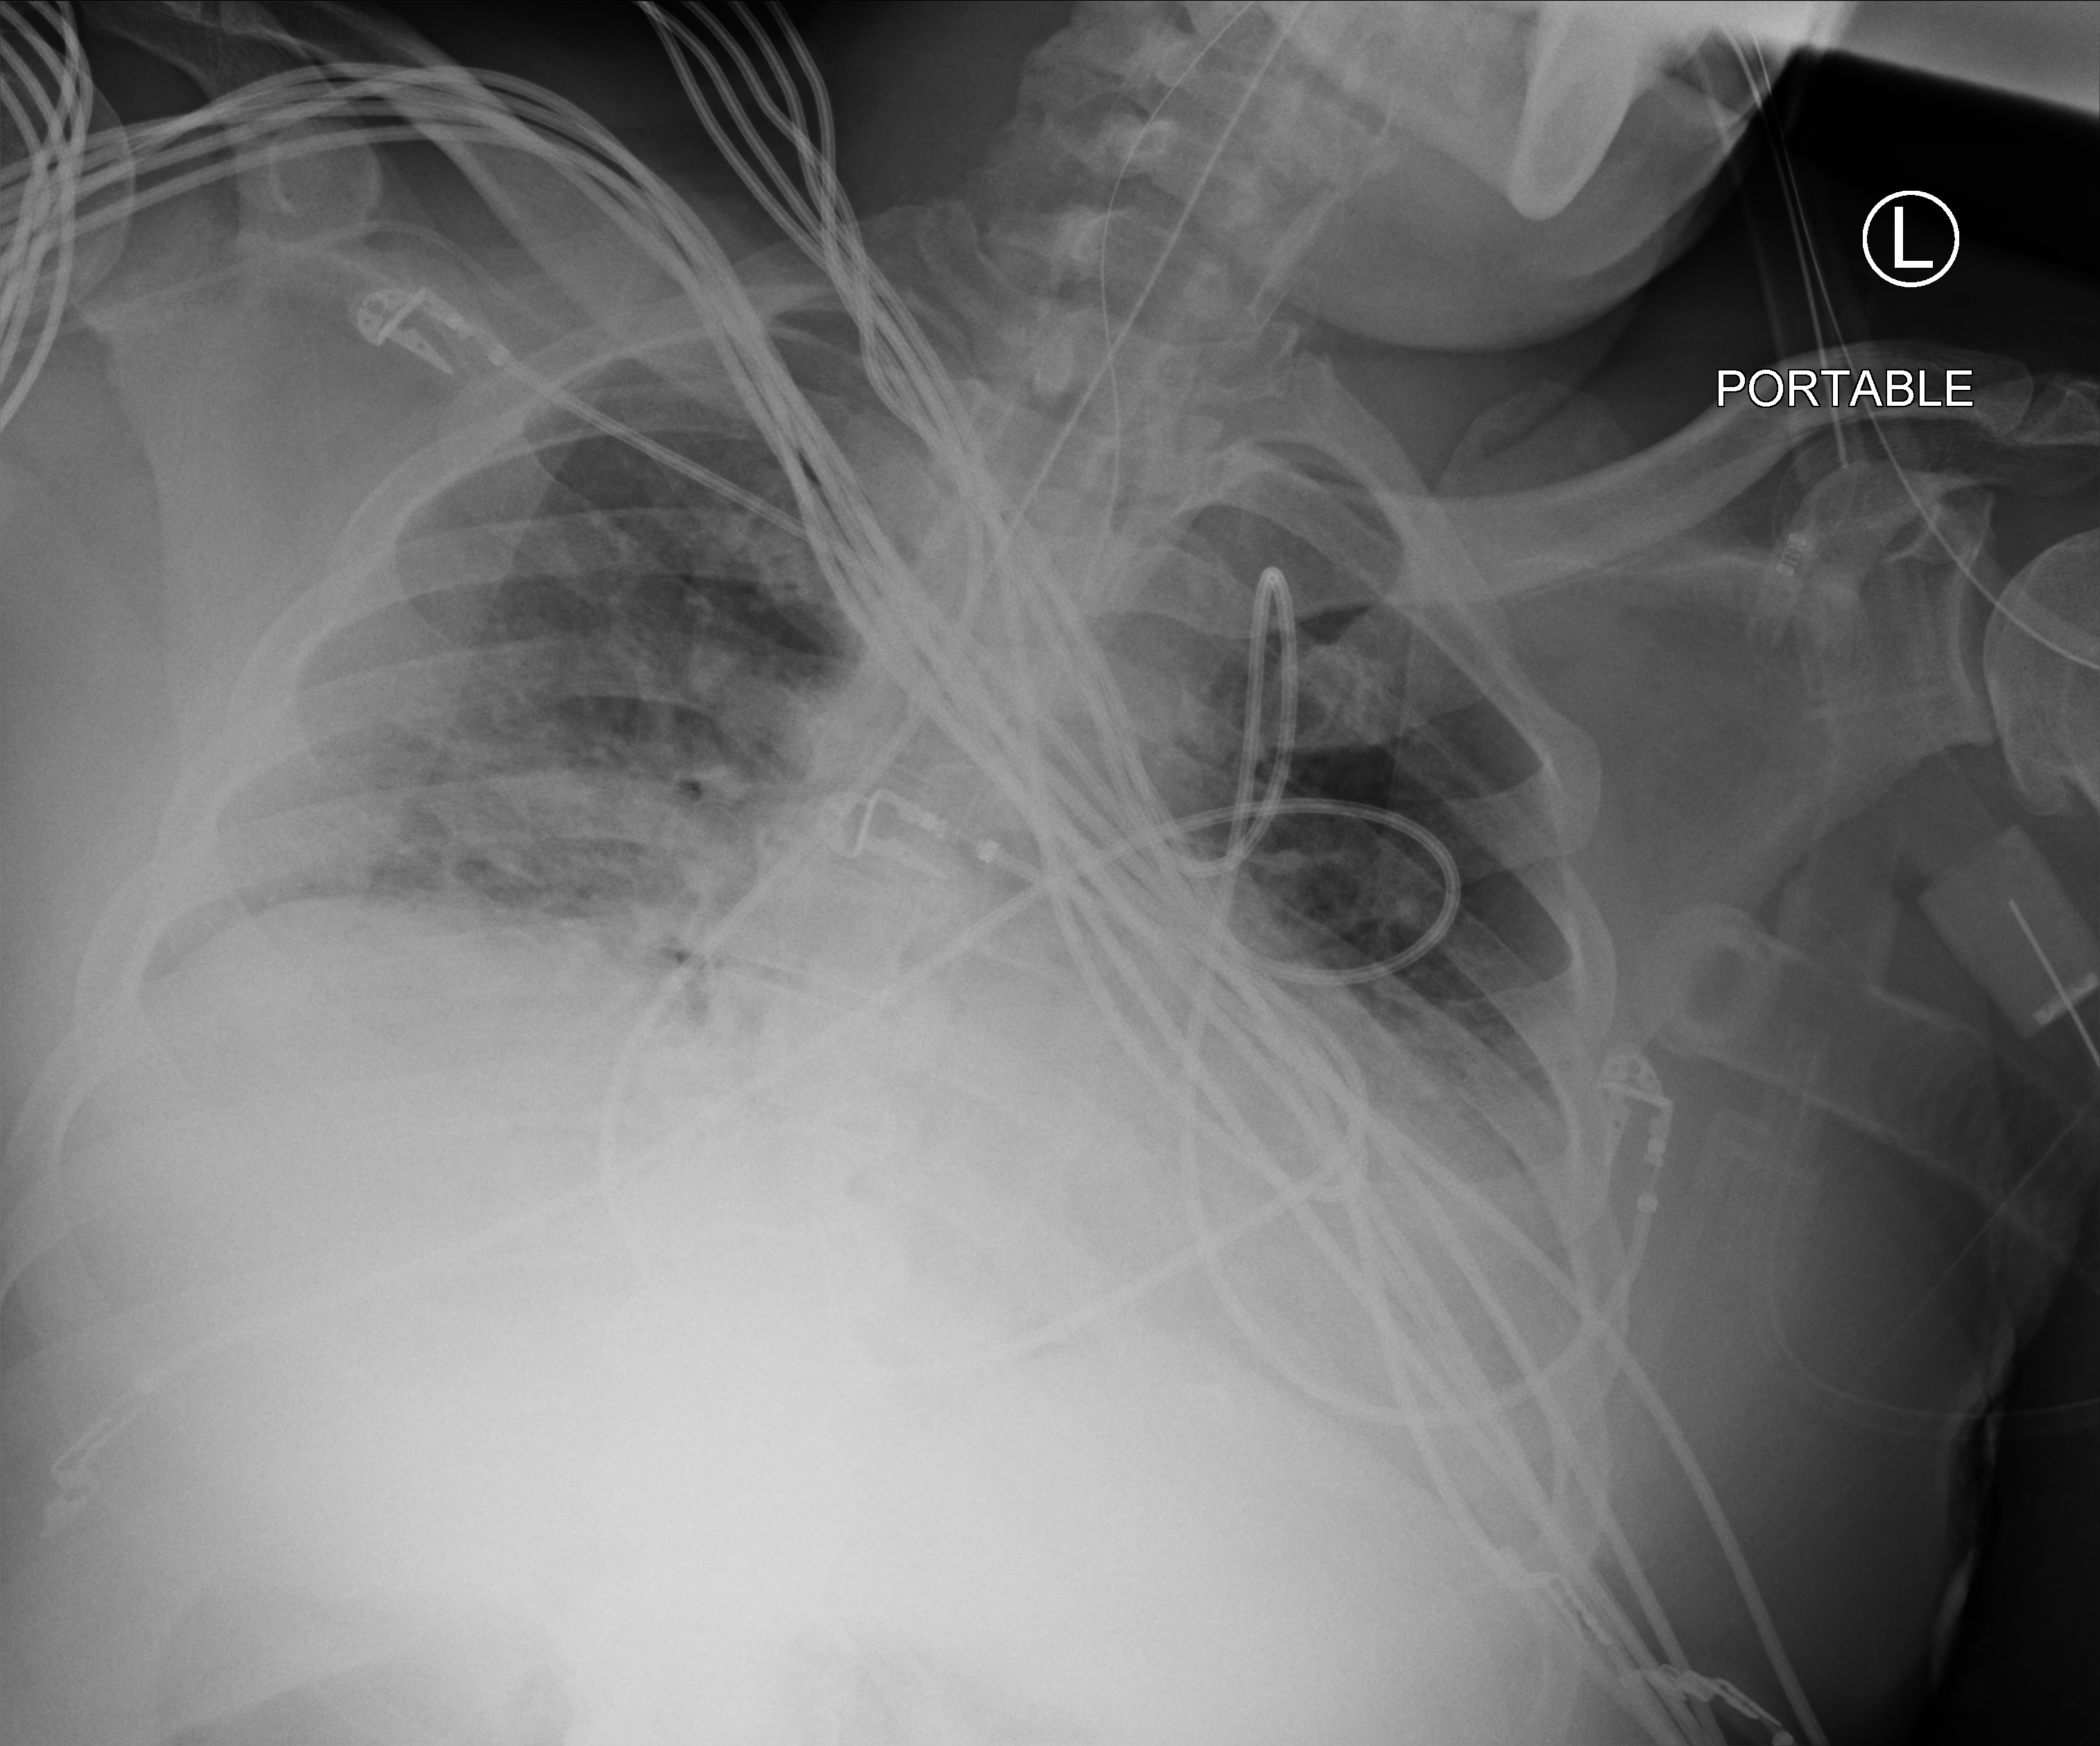
Bedside chest radiograph (computed radiography); anteroposterior (AP) projection. Patient hospitalised with COVID-19; male, aged 18–59 years.
Admission-level facts for this patient (not findings on this image; timing relative to this image not recorded):
- admitted to intensive care during this hospital stay: yes